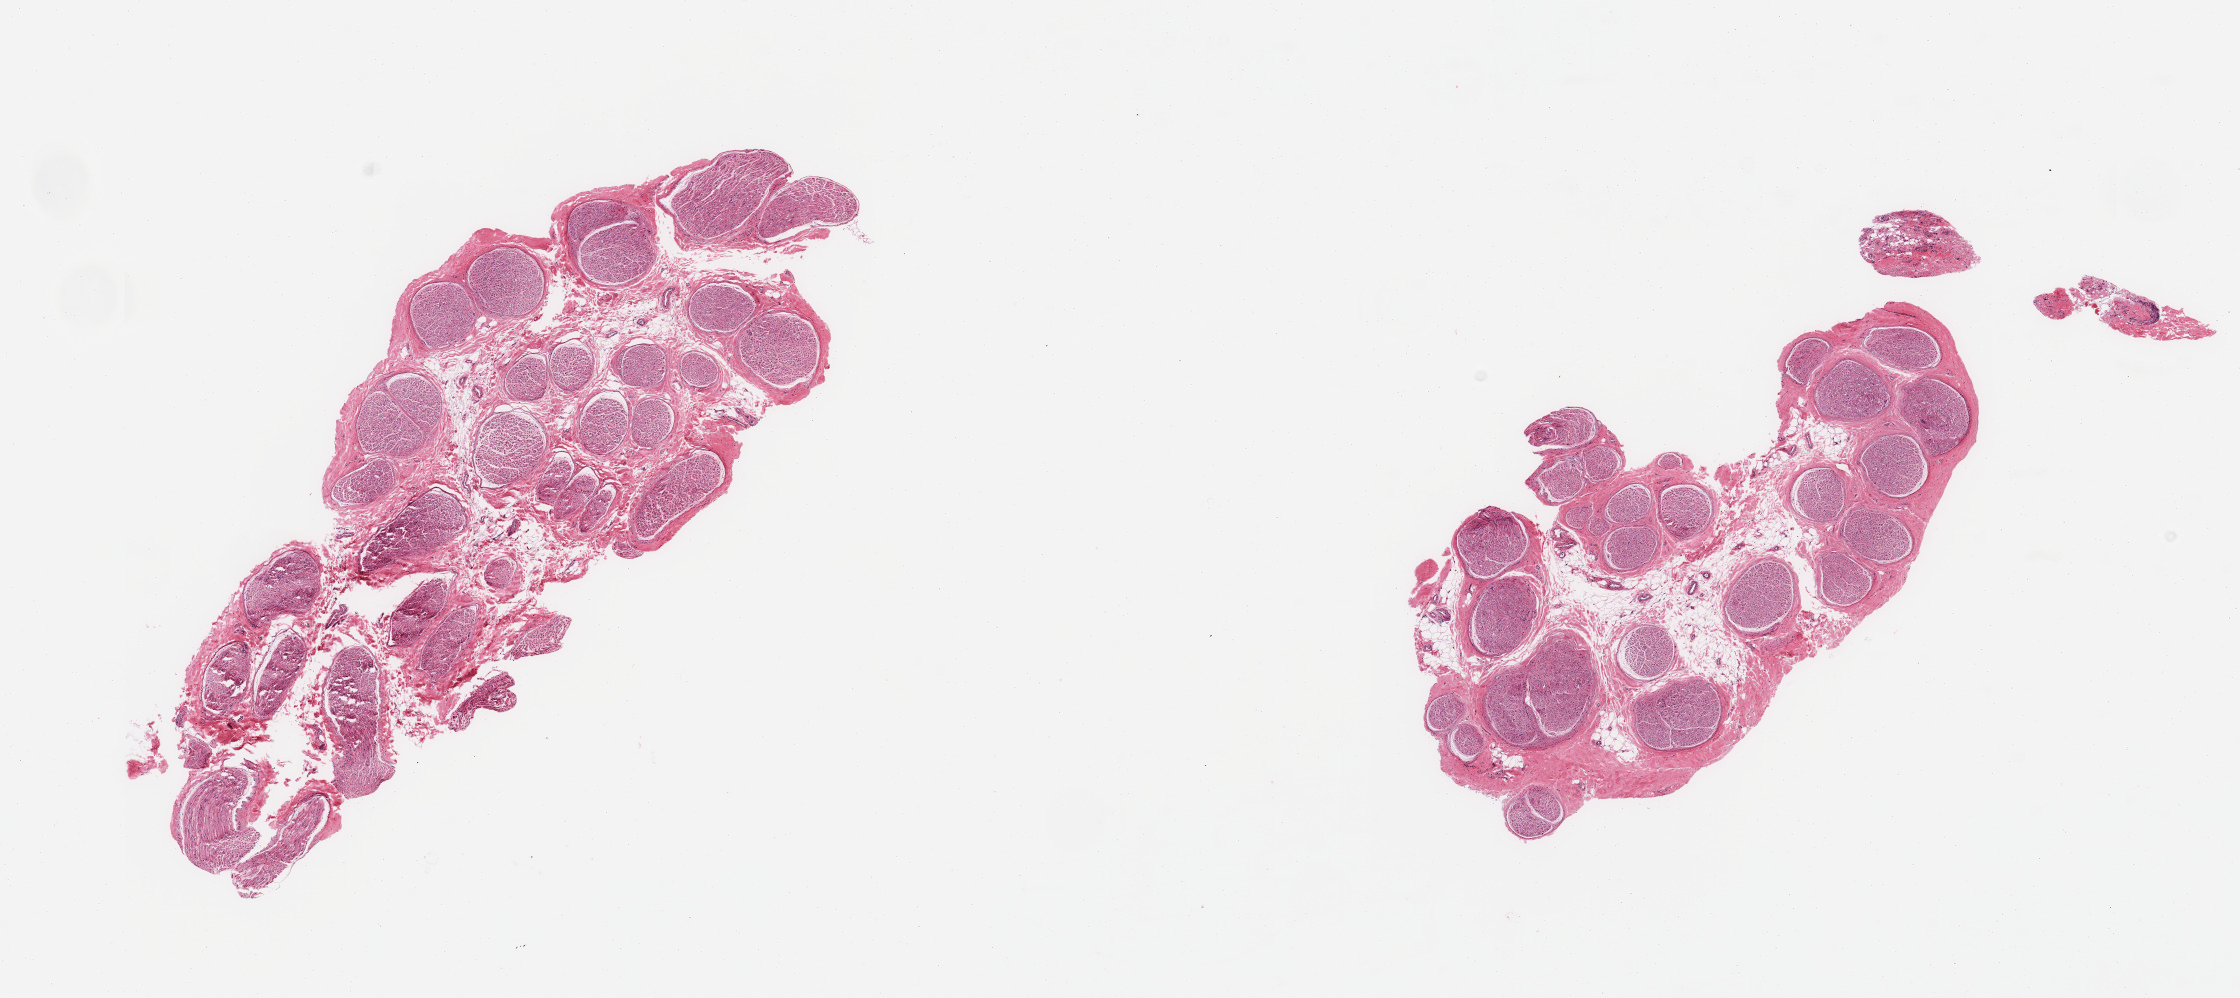
Whole-slide image, hematoxylin and eosin (H&E) stain, shown as a low-resolution overview of the whole scanned area (about 17.7 x 7.9 mm); PAXgene-fixed, paraffin-embedded tissue; sampled site (target tissue): tibial nerve; tissue donor sample. Donor: male.
* review note (as recorded): 2 pieces, no aderent fat